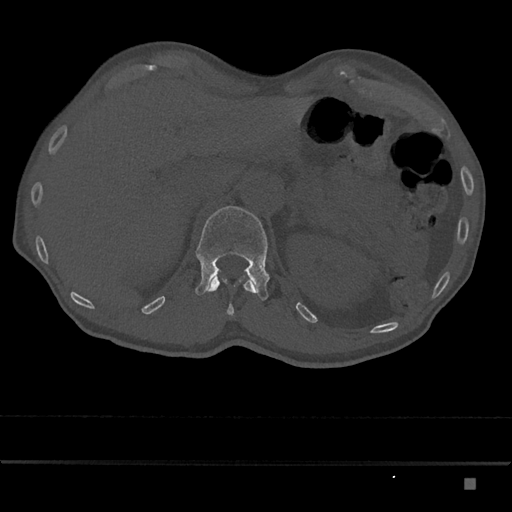
CT including the spine, one axial slice. Bone window (W 1800 / L 400 HU). 512 × 512 image matrix. Male patient, age 72 years. From the clinical record (not read from this slice): primary cancer: prostate.
Annotated regions visible in this slice (semi-automatic segmentation, software-assisted and operator-edited):
- L1 vertebra: box from (x=195, y=206) to (x=270, y=301) px
- T12 vertebra: (x=206, y=276)–(x=256, y=315)